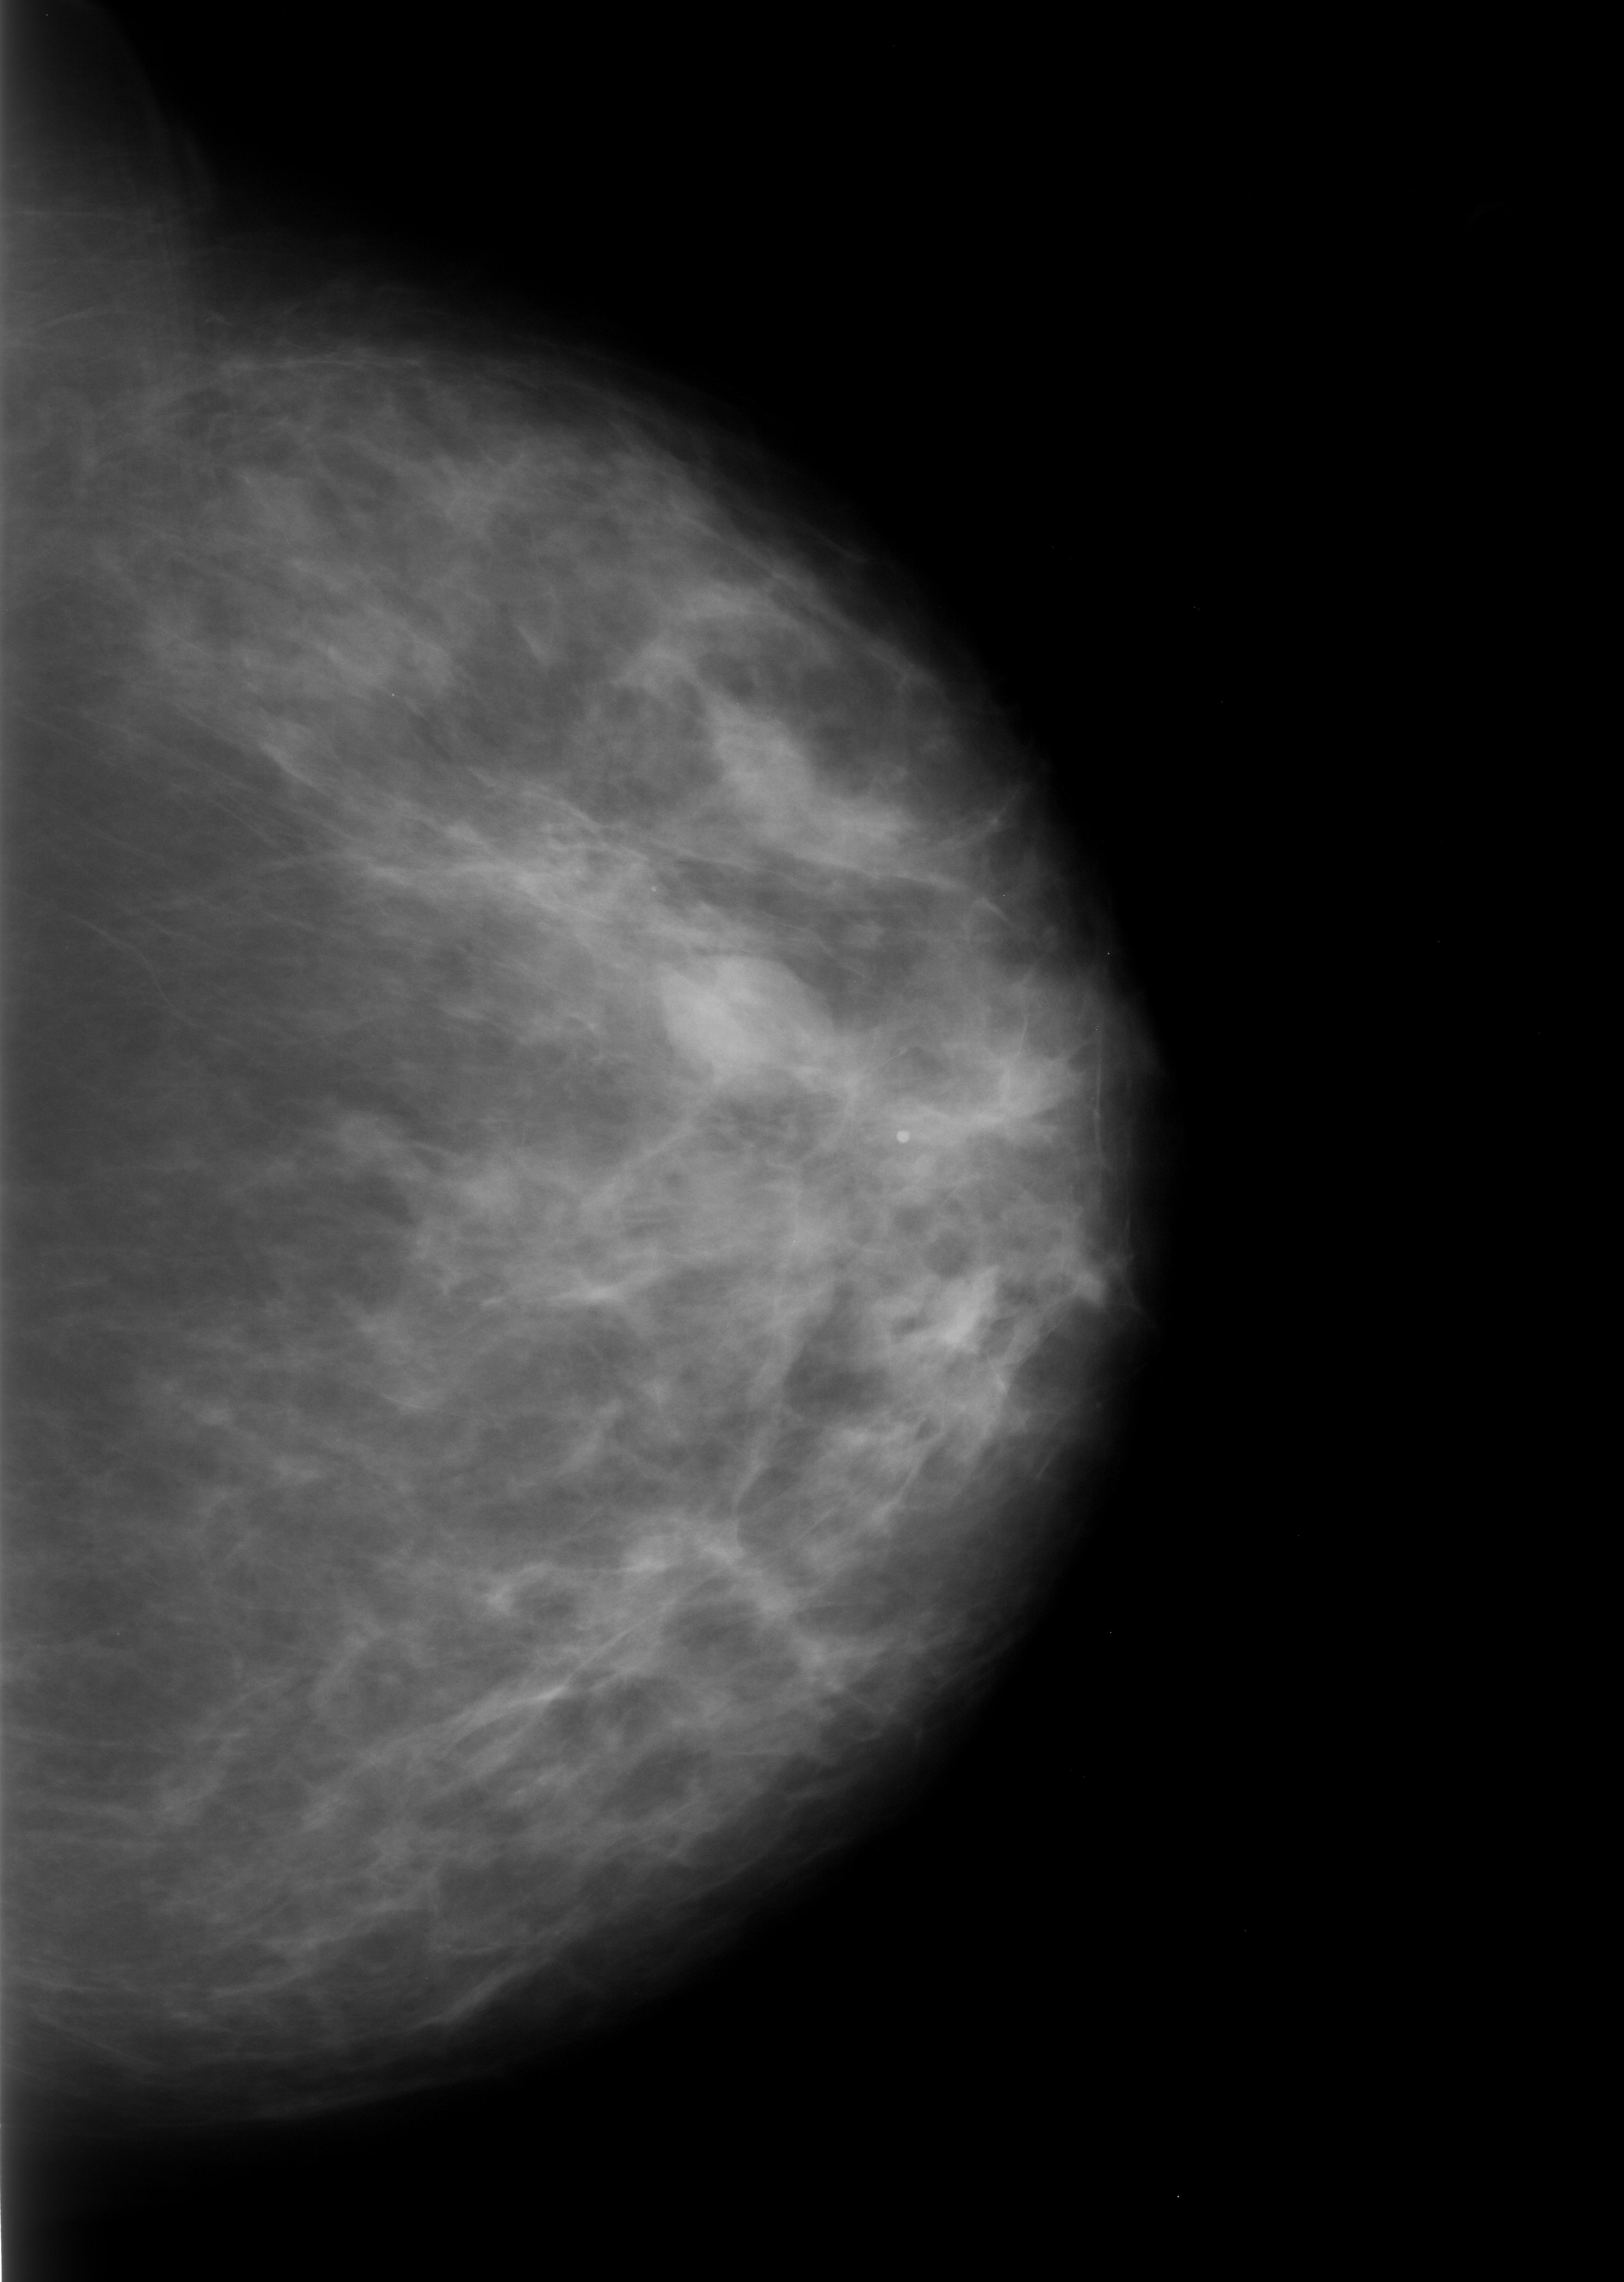
Mammogram (digitized film), left breast, CC view, breast composition: scattered fibroglandular densities (BI-RADS density category 2 of 4).
- Marked abnormality: mass, shape oval, margins circumscribed; BI-RADS assessment category 3; pathology result (as recorded, not read from the image): benign.